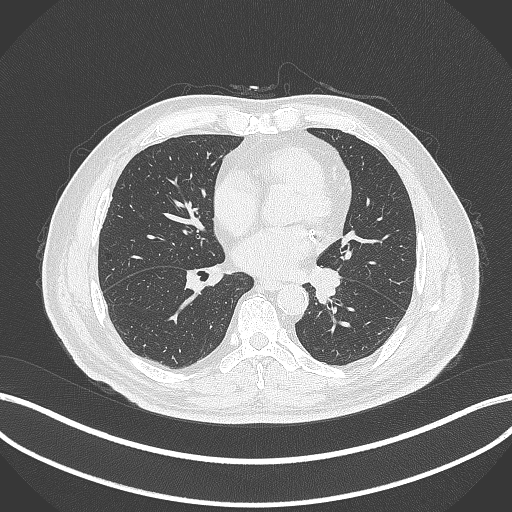
Chest CT, one axial slice; slice 126 of 312 in the series (ordered by position); reconstruction kernel B70f; 120 kVp; lung window (W 1500 / L -600 HU); 1 mm slice thickness; 512 × 512 image matrix, field of view 400 × 400 mm. Patient: male, 71 years. From the clinical record (not read from this slice): clinical TNM (as recorded): T1b N0 M0.
Structures marked on this image (rectangle marked by the reading radiologist):
- lung tumour (recorded histology: squamous cell carcinoma): box from (x=309, y=263) to (x=344, y=307) px